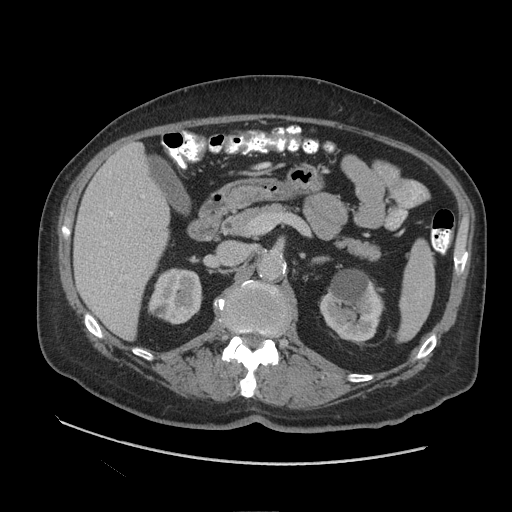
Contrast-enhanced abdominal CT (liver protocol), one axial slice. Slice 45 of 109 in the series (ordered by position). Reconstruction kernel STANDARD. 140 kVp. Soft-tissue window (W 400 / L 40 HU). 2.5 mm slice thickness. 512 × 512 image matrix, field of view 420 × 420 mm. Case-level facts recorded for this patient, not image findings: diagnosis: hepatocellular carcinoma (patient treated with transarterial chemoembolisation; whether this scan precedes or follows treatment is not stated here); TNM stage (as recorded): Stage-I; Child-Pugh class: A; tumour nodularity: uninodular.
Annotated regions visible in this slice (semi-automatic segmentation, software-assisted and operator-edited):
- liver parenchyma outside the tumour (the mass and vessels are separate outlines, so this box may not span the whole liver): bounding box <74,142,170,338> (left, top, right, bottom; pixels)
- liver vessels: <104,196,144,279>